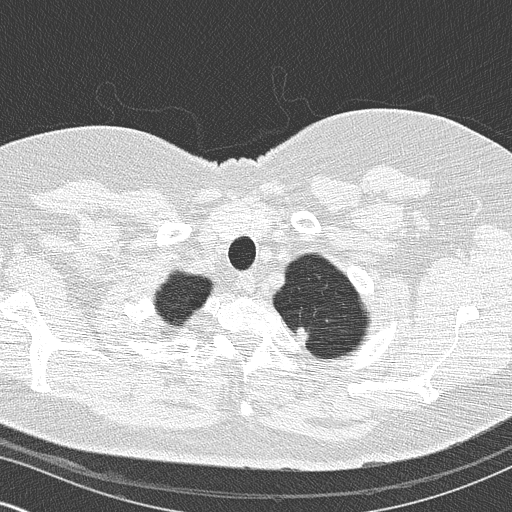
Chest CT (low-dose screening protocol), one axial image, second screening round (one year after baseline), lung window (W 1500 / L -600 HU), 2 mm slice thickness, slice 17 of 155 in the series, 512 × 512 image matrix. Female participant, aged 60 years at enrolment. Former smoker at enrolment.
Lesion marked by an expert reader, bounding box [x1, y1, x2, y2] px = [279, 318, 322, 358]. Screening reader's record for this exam: no non-calcified nodule ≥4 mm recorded. Official screen result: negative screen, minor abnormalities not suspicious for lung cancer. Lung cancer was diagnosed 464 days after this screen (after the third annual screen): non-small cell carcinoma, left upper lobe, poorly differentiated (G3), stage IB (AJCC 6th edition), 16 mm at pathology.